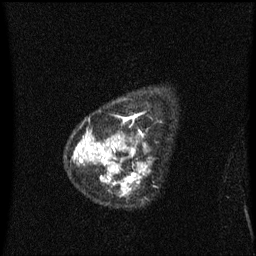
Breast MRI (dynamic contrast-enhanced), one sagittal slice; slice 49 of 60 in the series (ordered by position); dynamic contrast-enhanced series, image 2 of 3 at this slice position (ordered by acquisition); 1.5 T; TE 4.2 ms, TR 8.4 ms; 256 × 256 image matrix, field of view 200 × 200 mm. Female patient, age 48 years. From the clinical record (not read from this slice): setting: breast cancer imaged before/during neoadjuvant chemotherapy; receptor status: HR-positive, HER2-negative.
Annotated regions visible in this slice (semi-automatically segmented with operator editing):
- analysis volume of interest (the breast-tissue region the enhancement analysis was run in; not a lesion): bounding box <80,112,147,198> (left, top, right, bottom; pixels)
- tumour enhancement mask (voxels above the 70 % enhancement threshold inside the analysis volume of interest): <80,141,147,194>